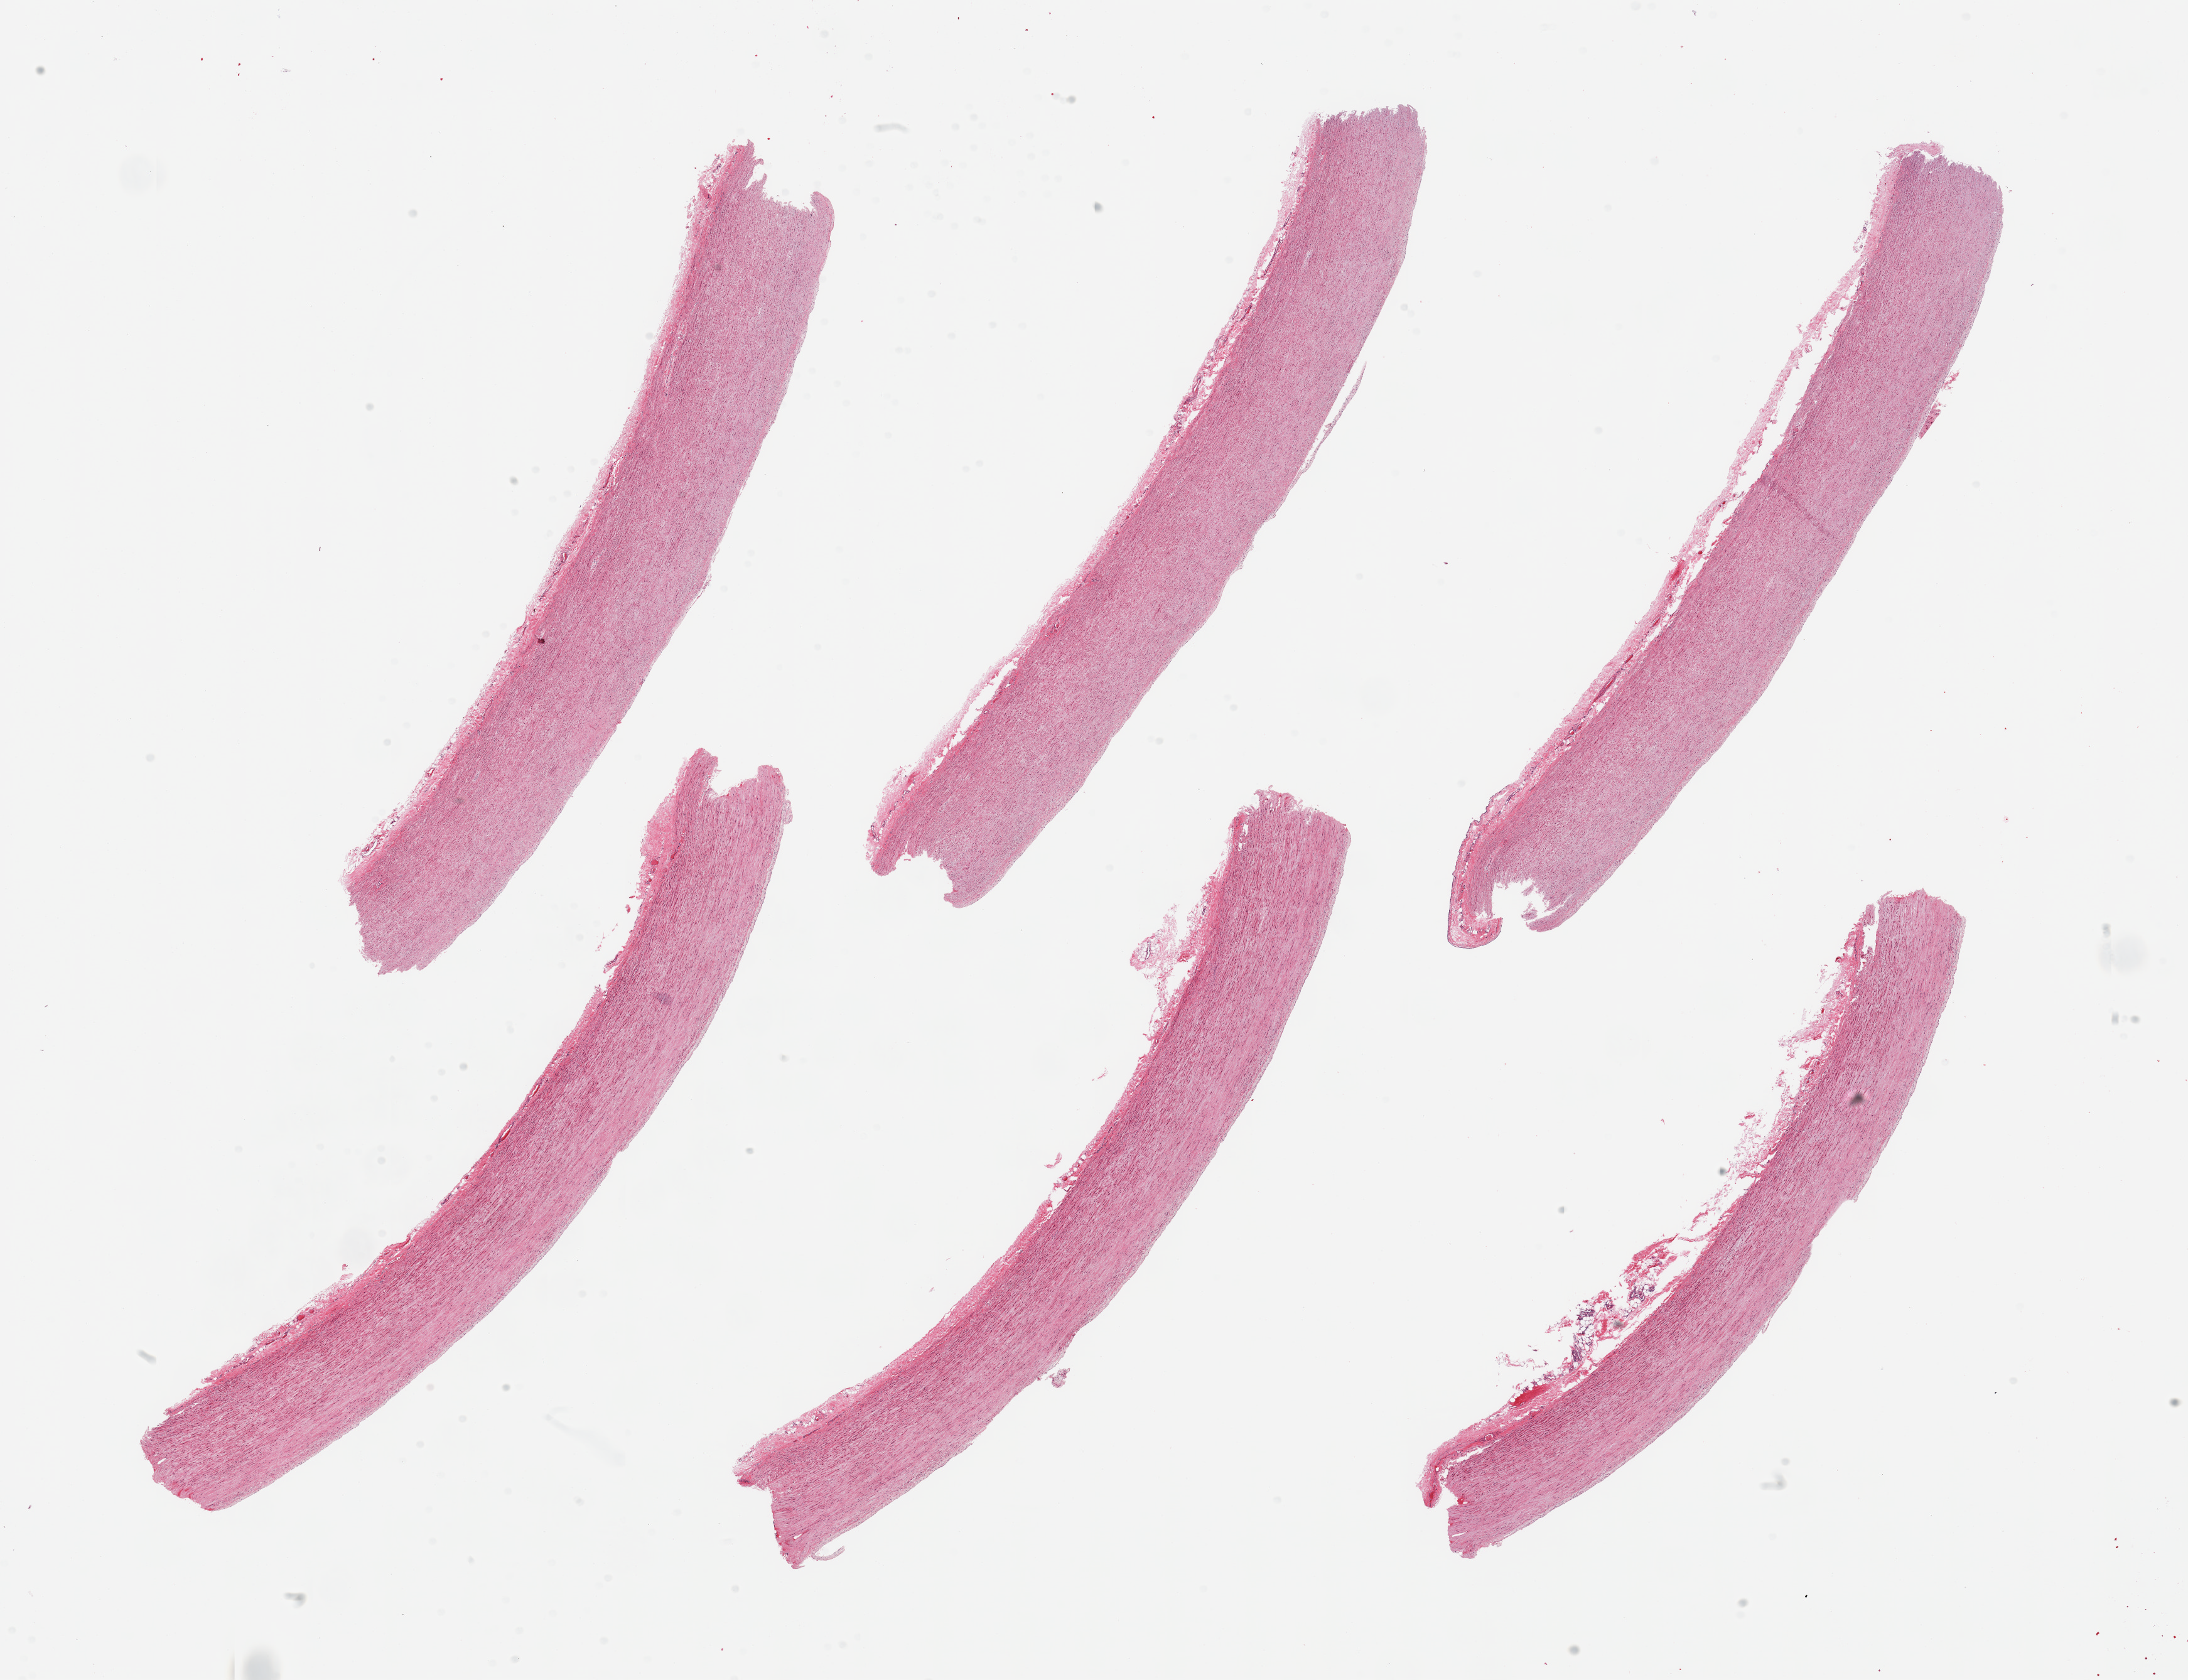
Whole-slide image, H&E stain — low-resolution overview of the scanned area, about 27.6 x 21.2 mm. PAXgene-fixed, paraffin-embedded tissue. Section of aorta (target tissue). Tissue donor sample. Donor: male.
Reviewer comment on this tissue sample: 6 pieces; no plaque formation, well trimmed.